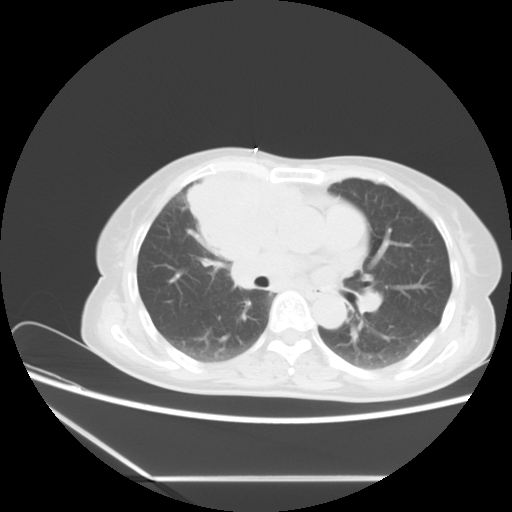
Chest CT, one axial slice; slice 8 of 16 in the series (ordered by position); reconstruction kernel STANDARD; 120 kVp; lung window (W 1500 / L -600 HU); 512 × 512 image matrix, field of view 350 × 350 mm. Female patient, age 63 years. From the clinical record (not read from this slice): clinical TNM (as recorded): T2b N1 M0.
Structures marked on this image (bounding box drawn by a radiologist):
- lung tumour (recorded histology: adenocarcinoma): bounding box <173,162,305,264> (left, top, right, bottom; pixels)